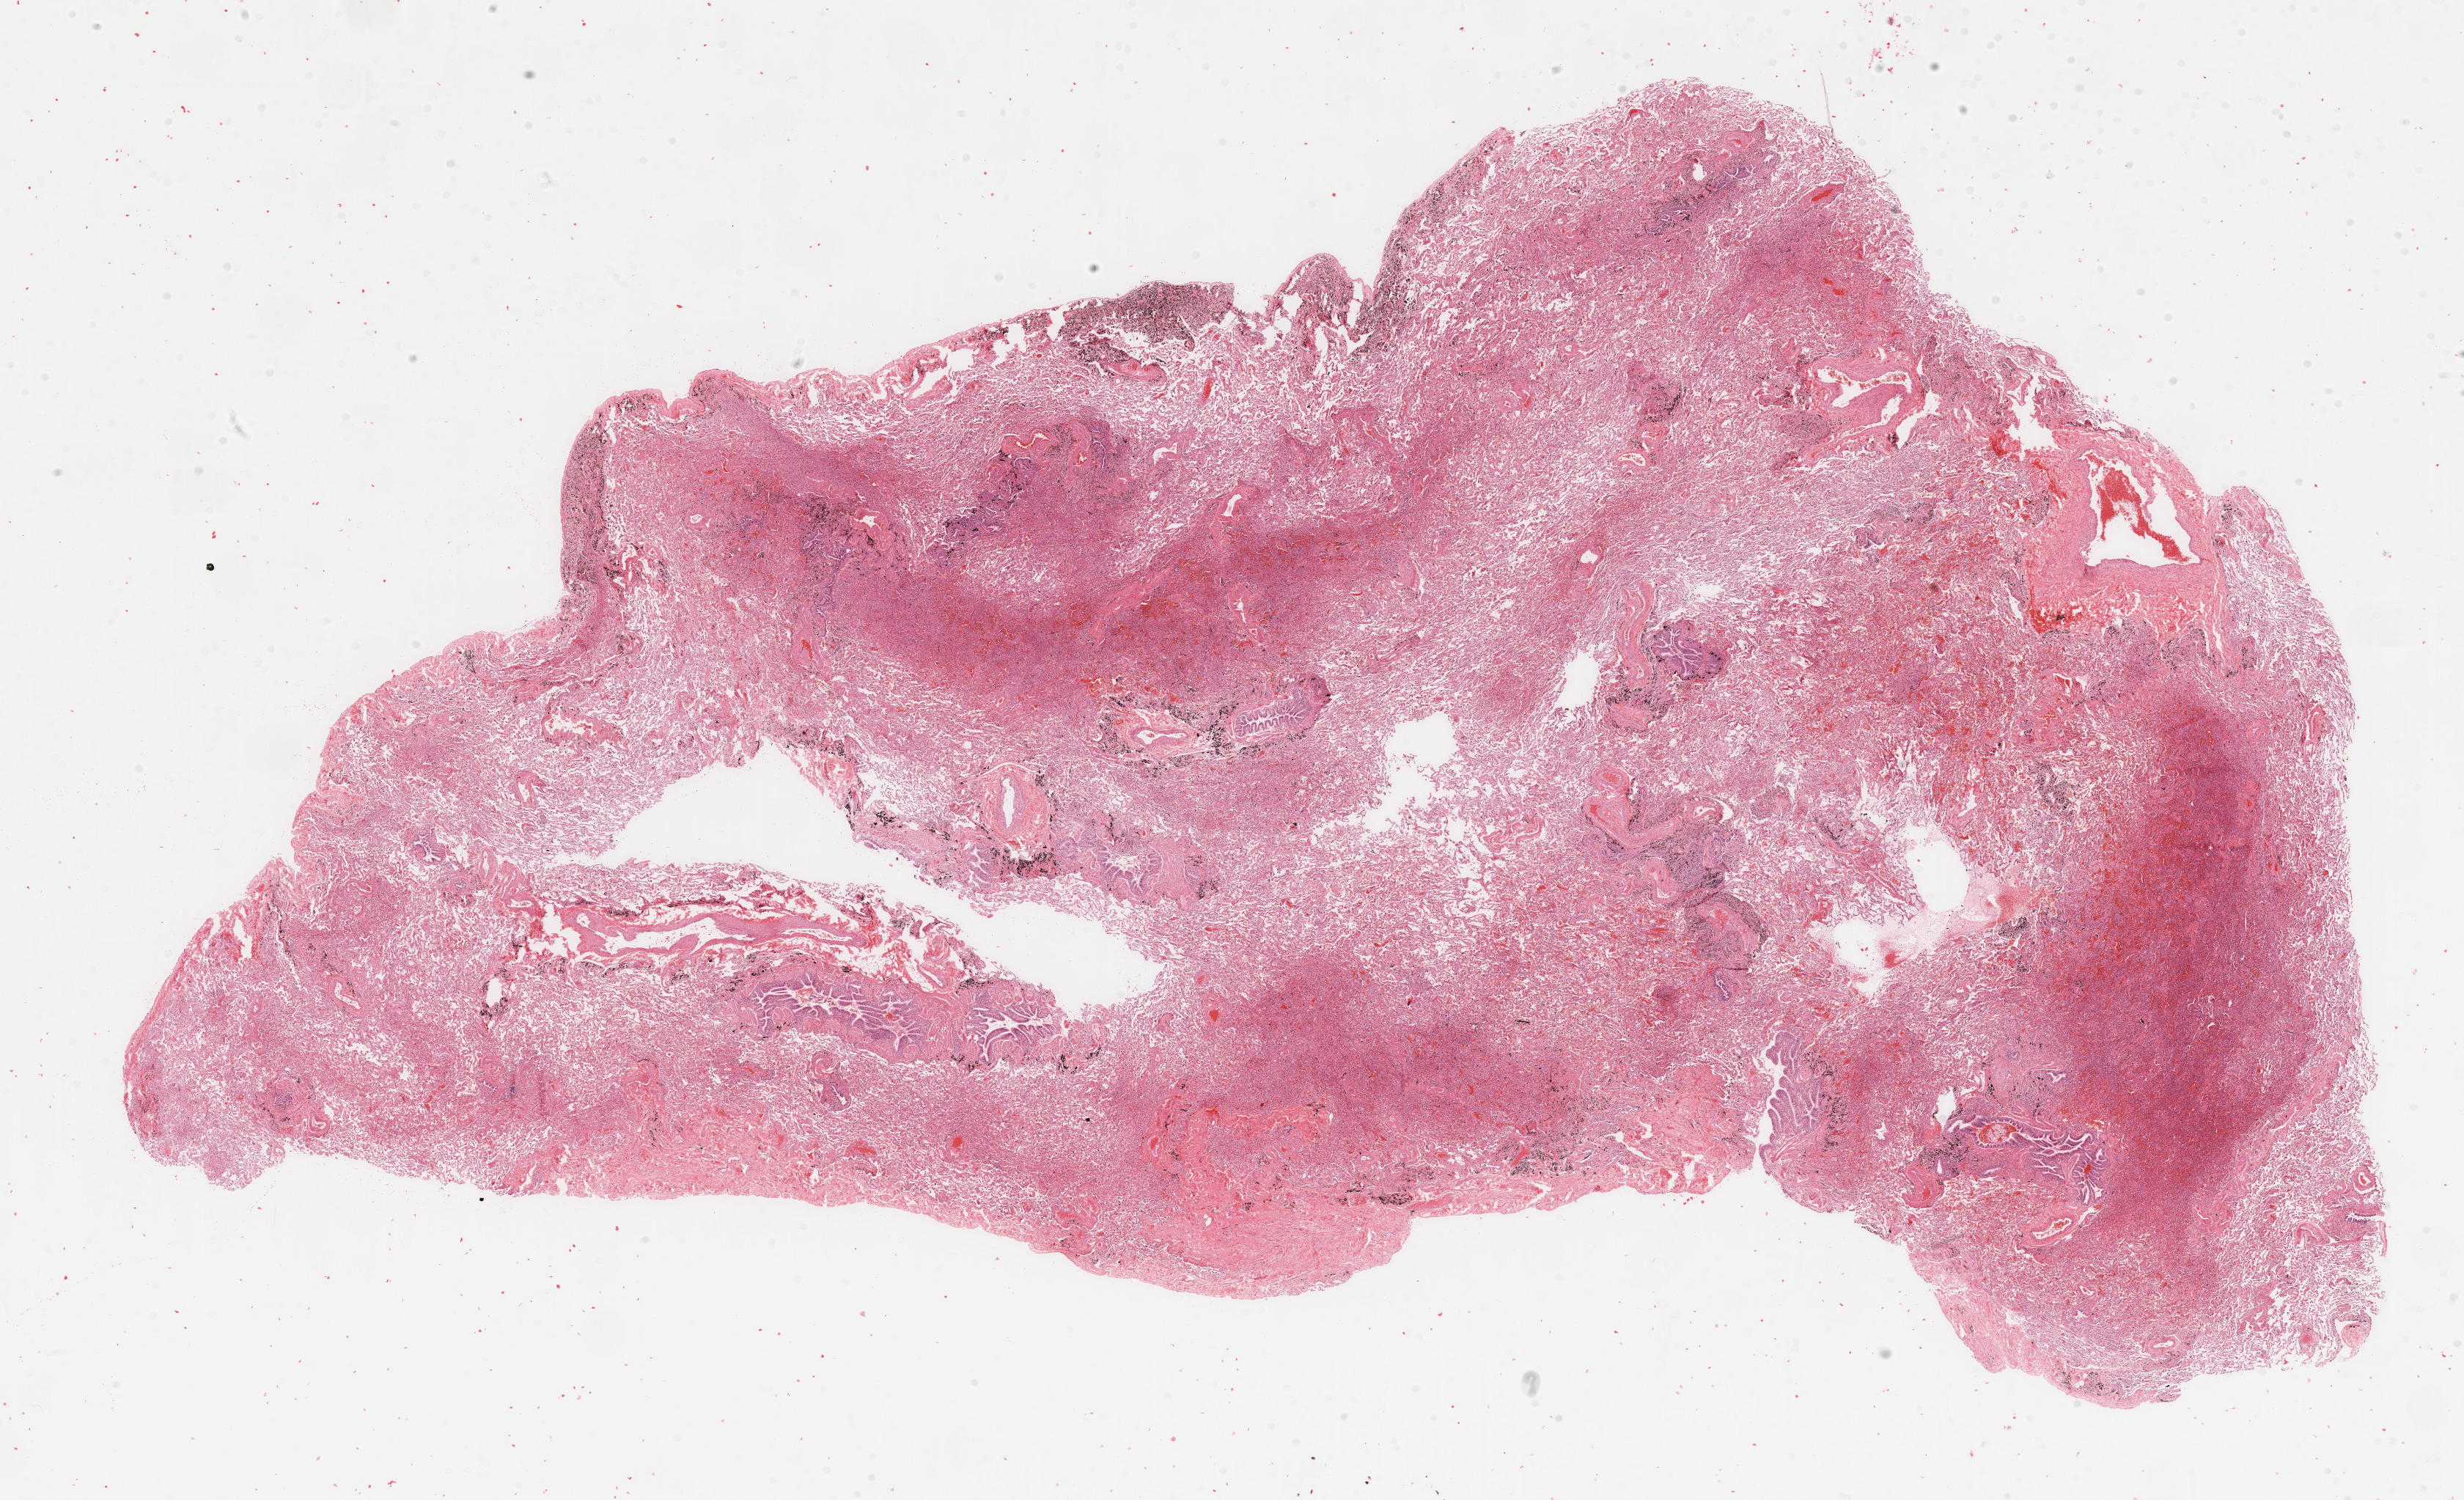
H&E whole-slide image, a low-resolution overview of the entire scanned area, about 26.6 x 16.2 mm (from a 20x scan); normal (non-tumour) tissue sample, sampled site: lung. 64-year-old male patient.
* this section: normal (non-tumour) tissue from the same patient
* patient diagnosis: Adenocarcinoma, NOS